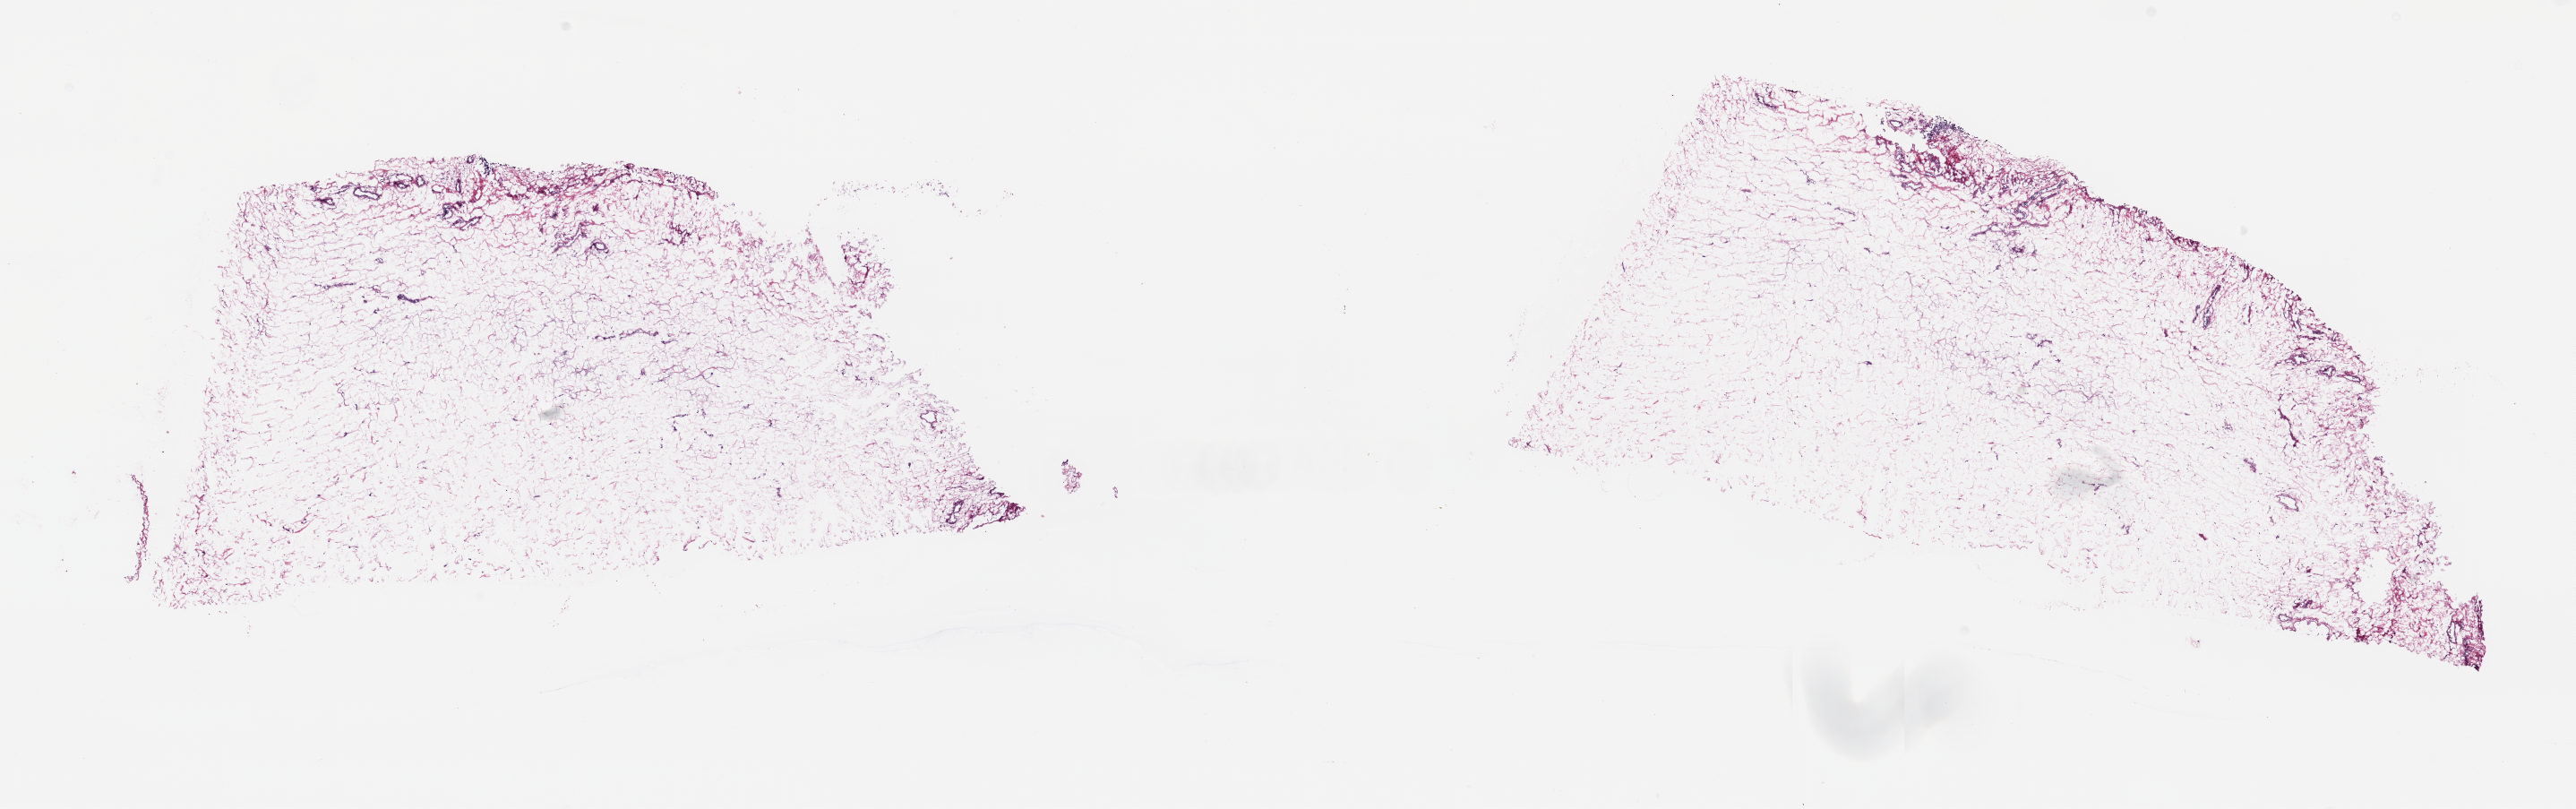
Whole-slide histology image, Hematoxylin and eosin (H&E) stained, shown as a low-resolution overview of the whole scanned area (about 22.8 x 7.2 mm, slide scanned at 20x). Frozen section from the top of the tissue portion. Sample: solid tissue normal (non-tumour tissue), bladder. Patient: male, age at initial diagnosis 54 years. Pathologist review of this section (percent, as recorded): tumour cells 0%, tumour nuclei 0%, normal cells 0%, stromal cells 100%, necrosis 0%. Inflammatory infiltration, as recorded: lymphocyte infiltration 0%, monocyte infiltration 0%, neutrophil infiltration 0%.
• this section: solid tissue normal (non-tumour) sample from the same patient
• patient diagnosis: Transitional cell carcinoma (dome of bladder)